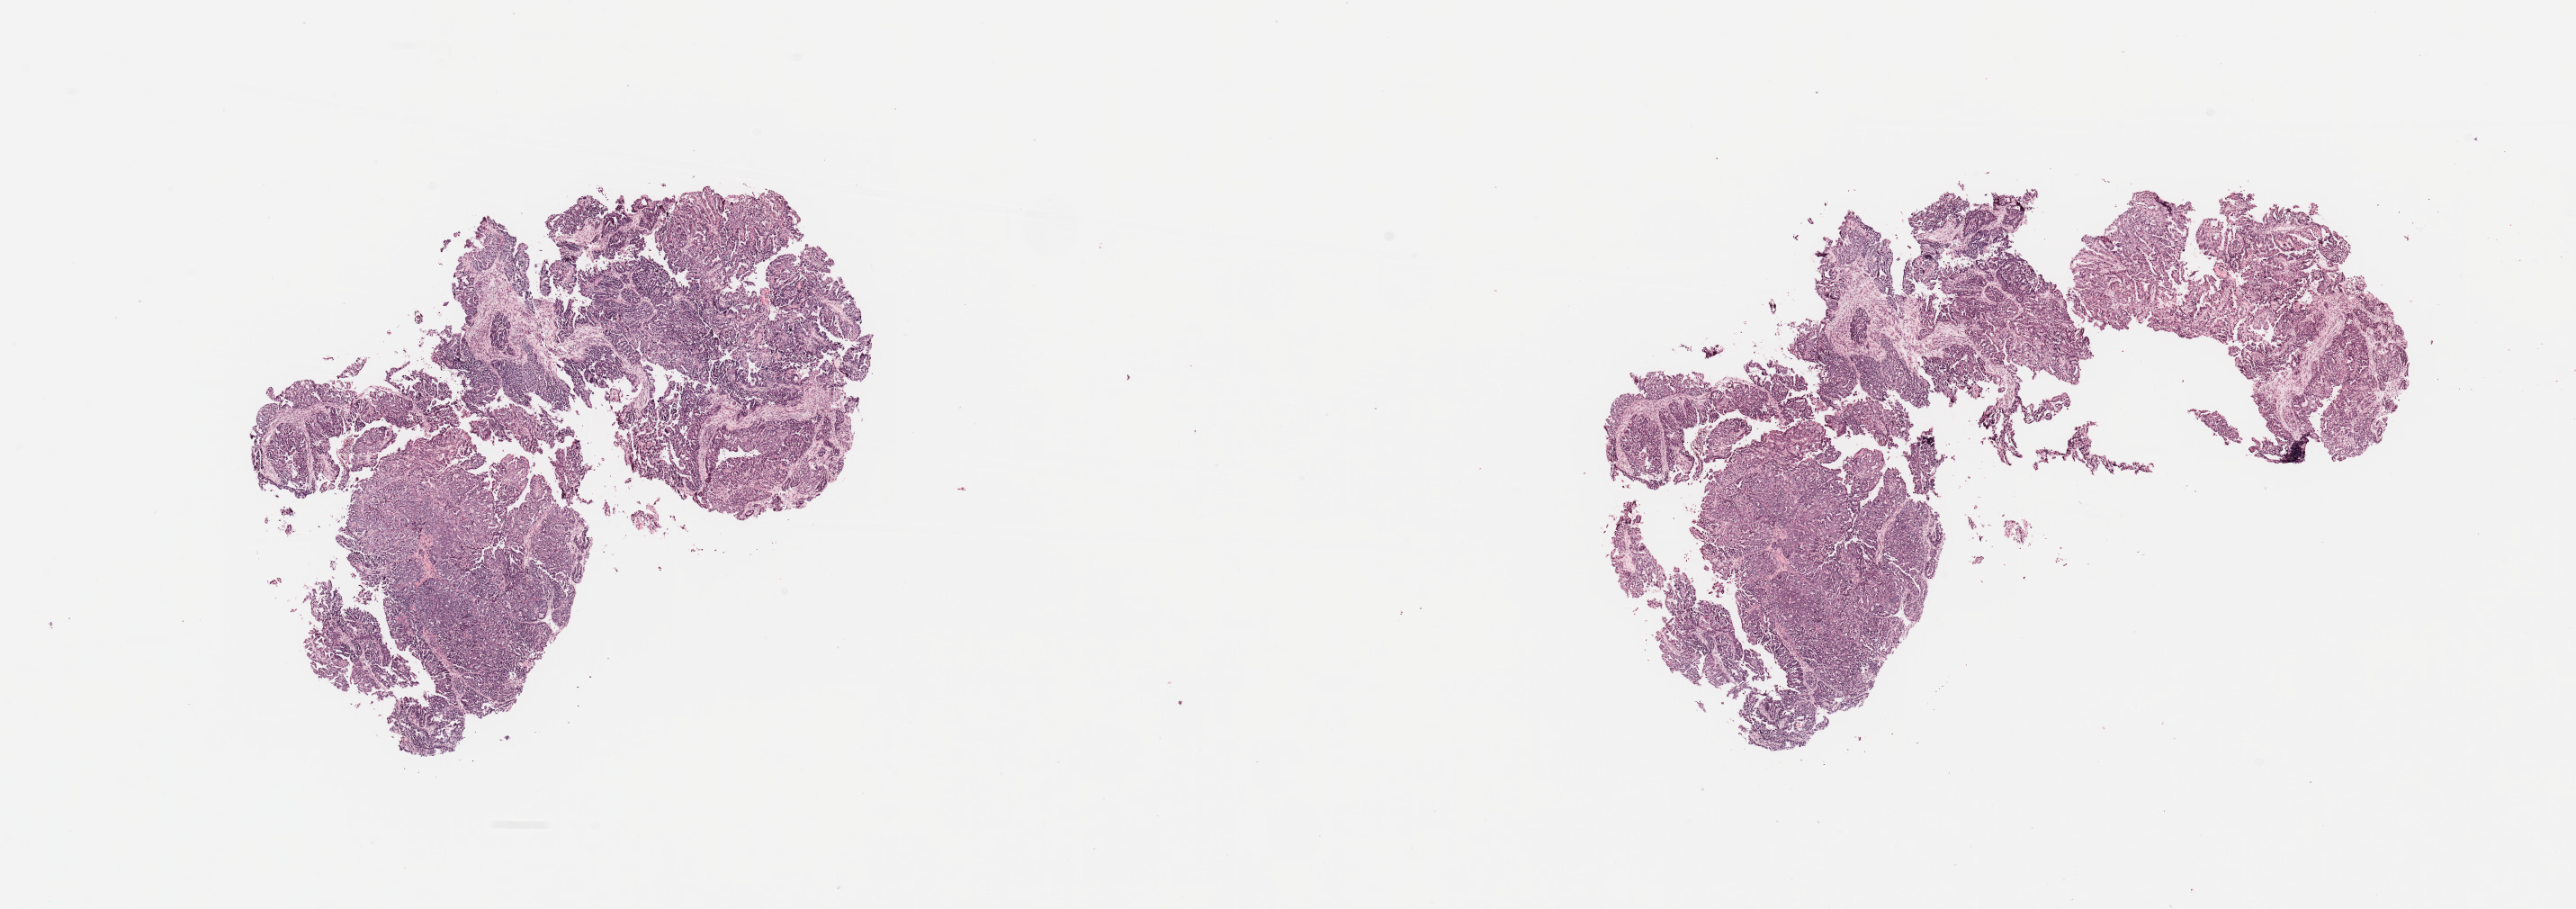
Whole-slide histology image, Hematoxylin and eosin (H&E) stained — a low-resolution overview of the entire scanned area, about 22.6 x 8.0 mm (acquisition: 20x scan), uterus, tumour tissue. 81-year-old female patient.
Patient diagnosis (cohort enrolment): corpus endometrial carcinoma (uterus).